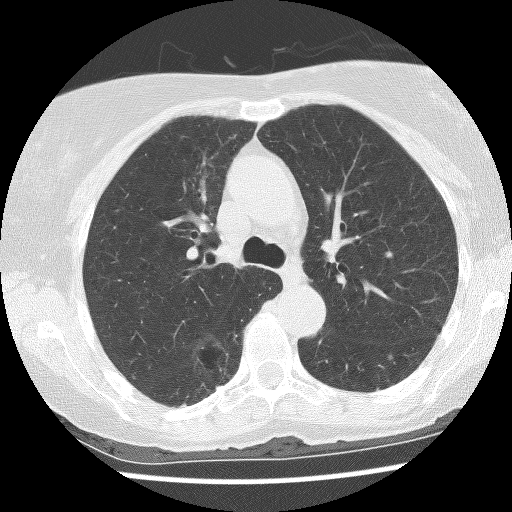
Low-dose screening chest CT, axial slice; baseline annual screen; lung window (W 1500 / L -600 HU); 2.5 mm slice thickness; slice 41 of 136 in the series; 512 × 512 image matrix, field of view 300 × 300 mm. Female, age 69 years at enrolment.
Lesion marked by an expert reader, box from (x=172, y=323) to (x=244, y=397) px. The screening reader recorded 2 non-calcified nodules or masses ≥4 mm on this exam (right lower lobe, right lower lobe); which of them this box marks is not recorded. Lung cancer was diagnosed 288 days after this screen: non-small cell carcinoma, right lower lobe, poorly differentiated (G3), stage IB (AJCC 6th edition), 36 mm at pathology.